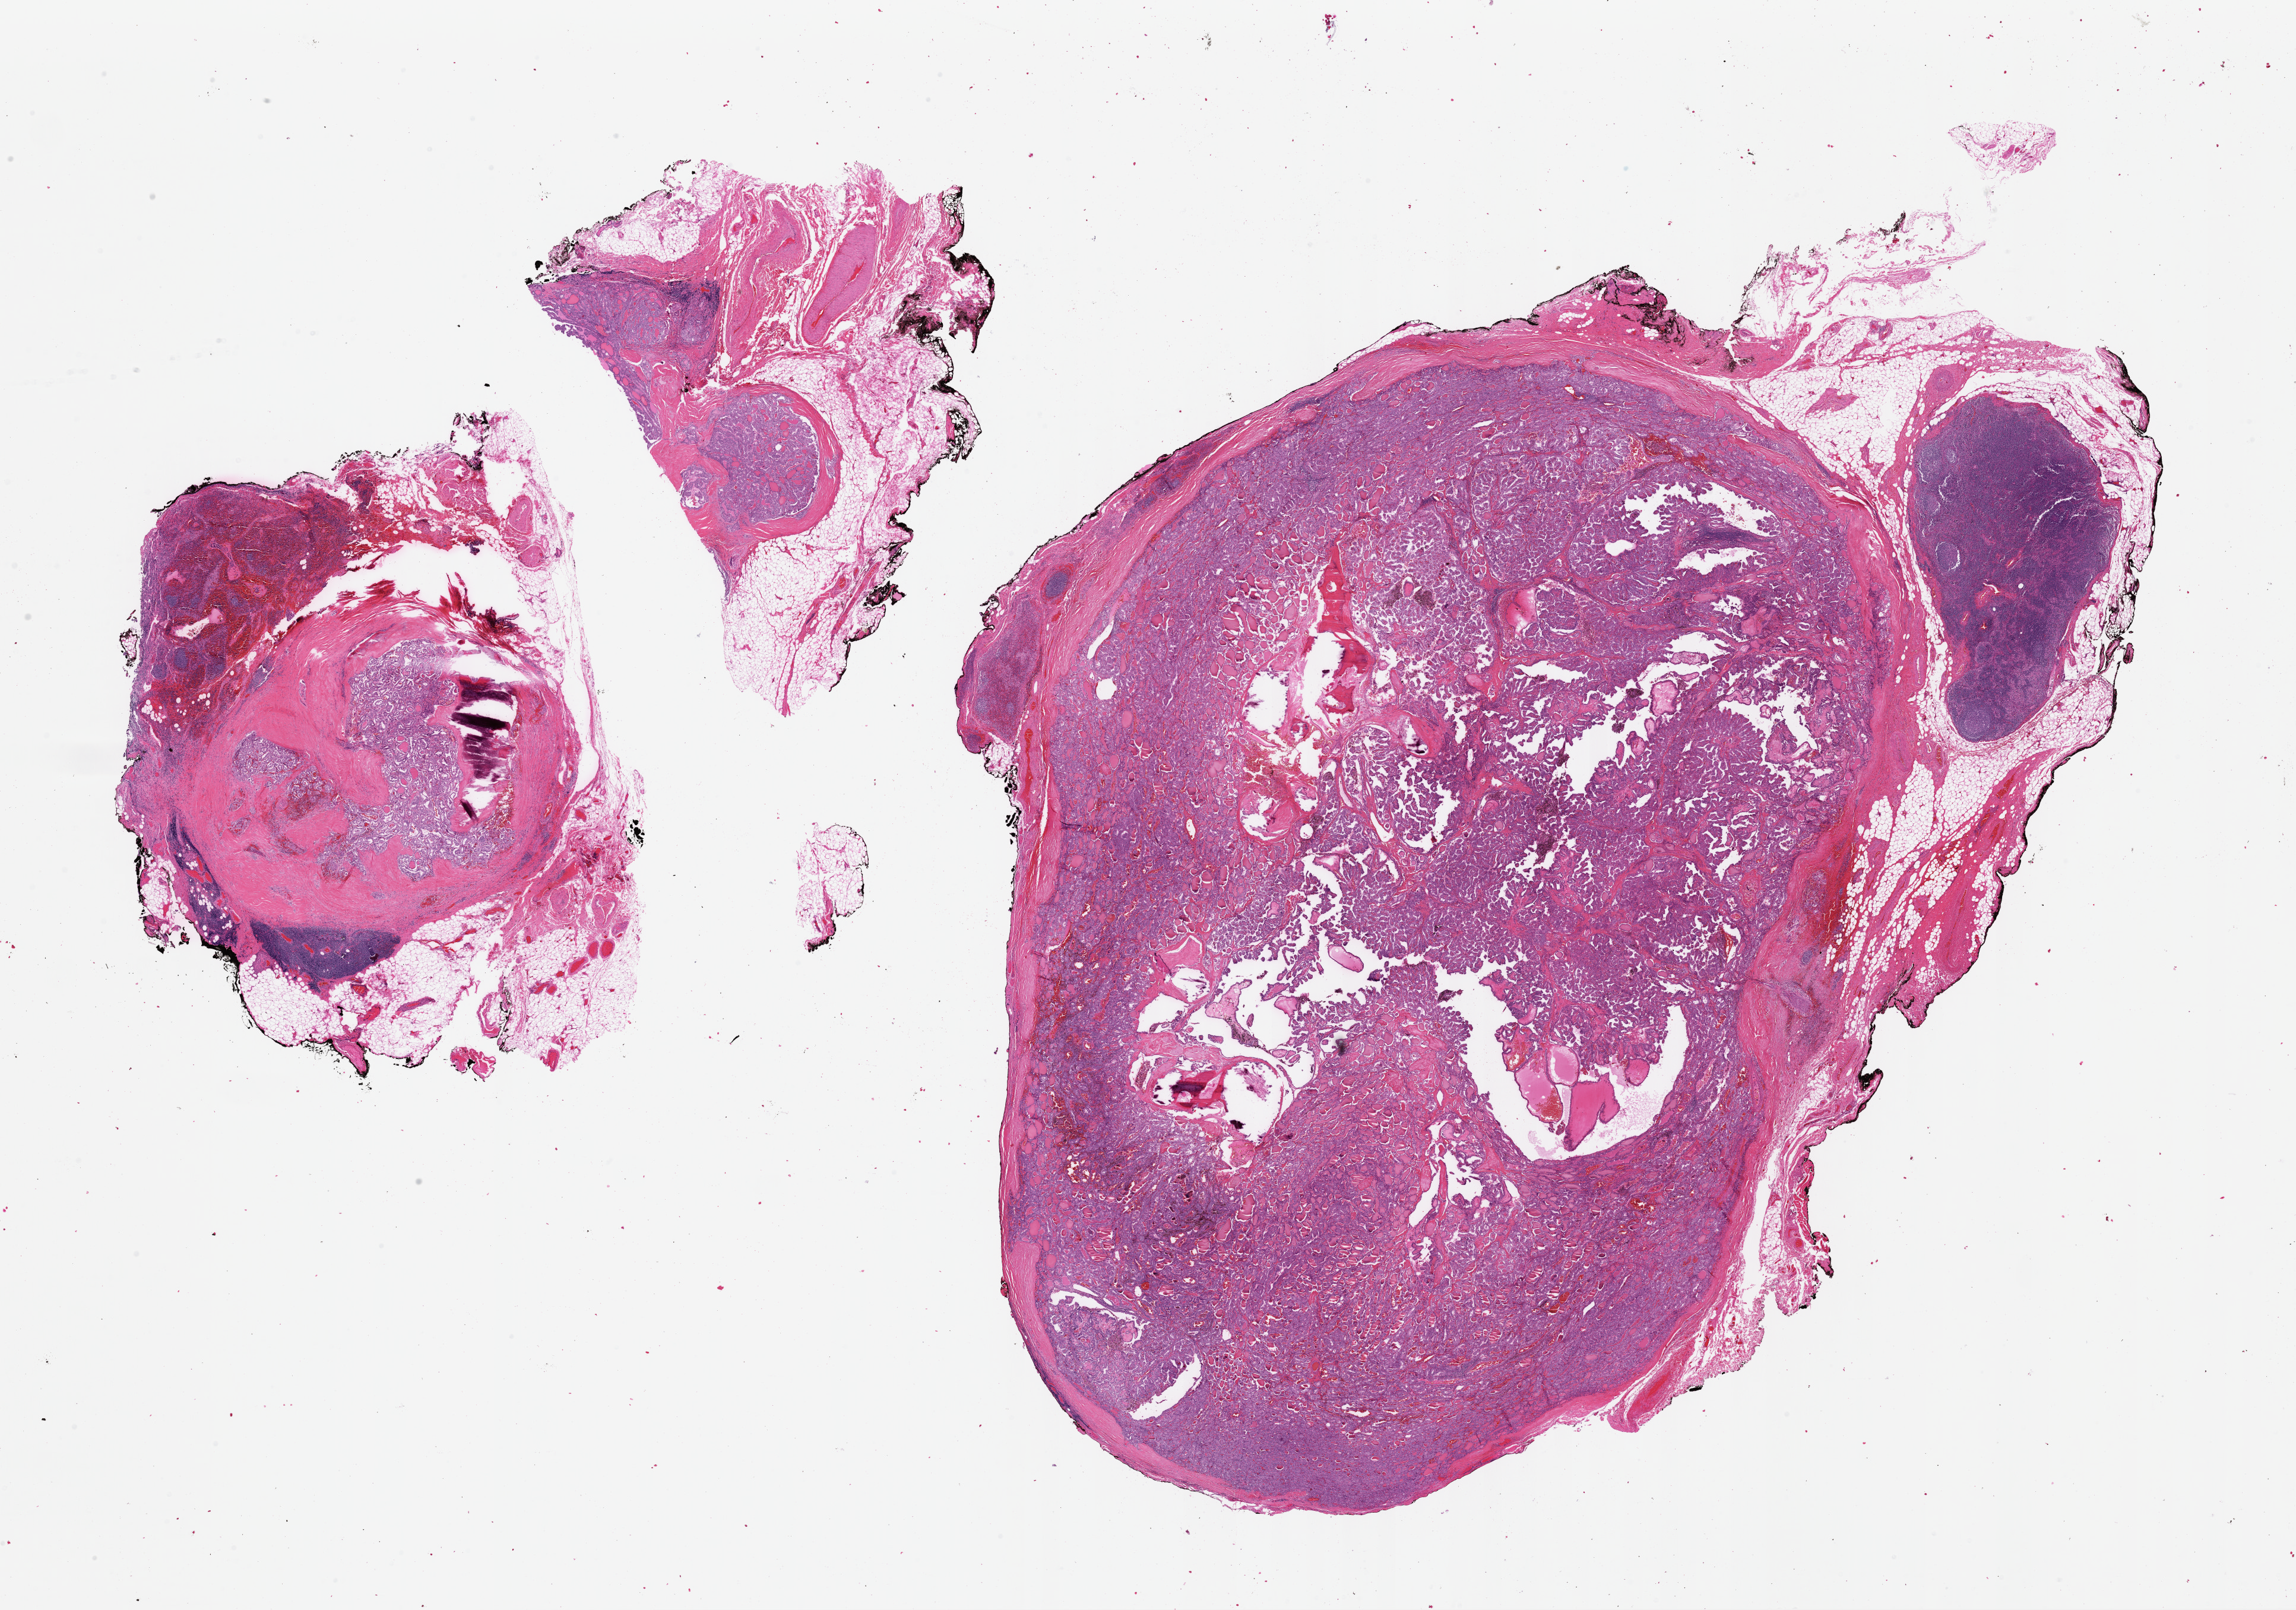
Whole-slide histology image, H&E-stained — low-resolution overview of the scanned area, about 30.5 x 21.4 mm; formalin-fixed paraffin-embedded (FFPE) diagnostic section; sample: primary tumour, thyroid. Female patient; age at initial diagnosis 48 years.
• AJCC pathologic stage: III (6th edition)
• lymph nodes positive (case pathology): 11 of 14 examined
• laterality: left
• histologic diagnosis: Papillary adenocarcinoma, NOS (thyroid gland)